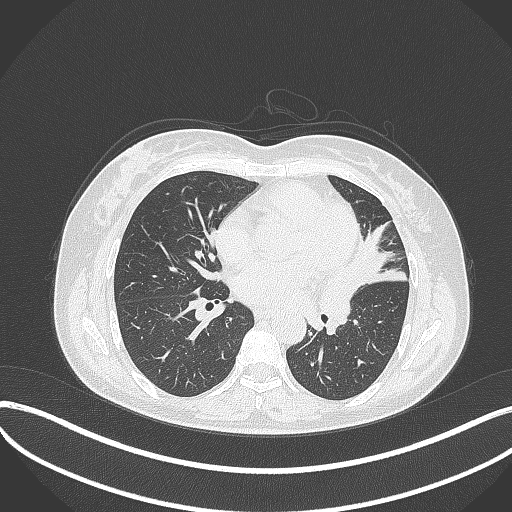
Chest CT, one axial slice; slice 167 of 373 in the series (ordered by position); reconstruction kernel B70f; lung window (W 1500 / L -600 HU); 1 mm slice thickness; 512 × 512 image matrix. Patient: female, 54 years. From the clinical record (not read from this slice): clinical TNM (as recorded): T2a N1 M0; histopathological grade: G3.
Annotated regions visible in this slice (bounding box drawn by a radiologist):
- lung tumour (recorded histology: small cell carcinoma): bounding box (x1, y1, x2, y2) in pixels: (317, 264, 358, 336)